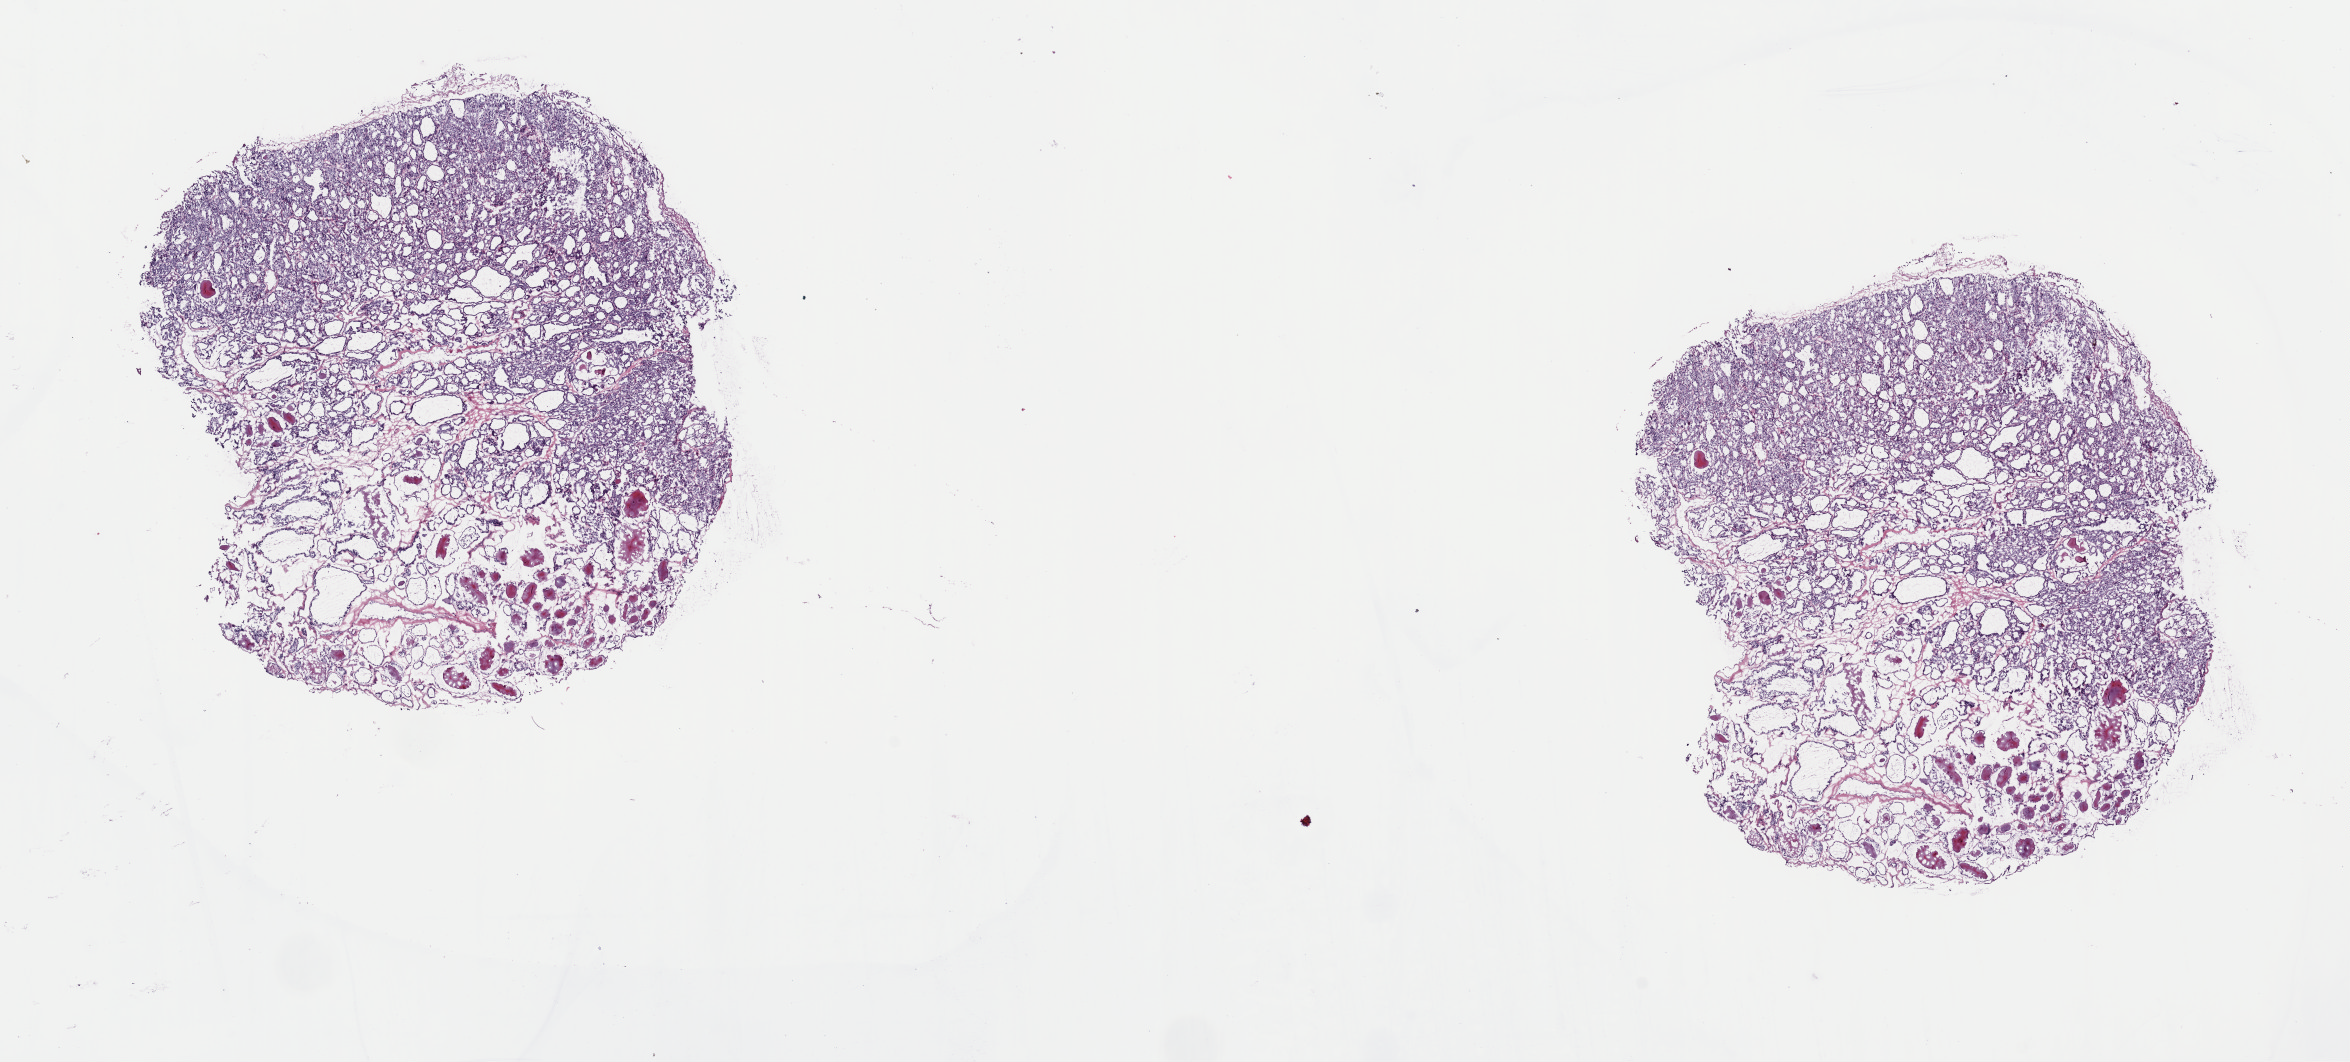
Digitized Hematoxylin and eosin (H&E) stained tissue section (whole slide) — low-resolution overview of the scanned area, about 18.6 x 8.4 mm (slide scanned at 40x), frozen section from the top of the tissue portion, thyroid, primary tumour sample. Patient: male, age at initial diagnosis 69 years. Slide review estimates, as recorded: tumour cells 100%, tumour nuclei 80%, normal cells 0%, stromal cells 0%, necrosis 0%. Inflammatory infiltration, as recorded: lymphocyte infiltration 2%, monocyte infiltration 1%, neutrophil infiltration 0%.
AJCC pathologic stage: III (7th edition). Pathologic diagnosis: Papillary carcinoma, follicular variant (thyroid gland).